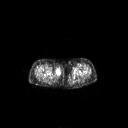
FDG PET of an extremity soft-tissue mass (from a PET/CT study), one axial slice. 3.27 mm slice thickness. 128 × 128 image matrix, field of view 700 × 700 mm. Patient: female, 78 years. Case-level facts recorded for this patient, not image findings: histological type: leiomyosarcoma; grade: intermediate; site of the primary tumour: parascapusular.
Structures marked on this image (expert contour drawn on MRI and transferred to this co-registered scan by the dataset authors):
- gross tumour volume including surrounding oedema: bounding box [x1, y1, x2, y2] px = [54, 67, 61, 75]
- gross tumour volume (mass): [54, 69, 61, 75]